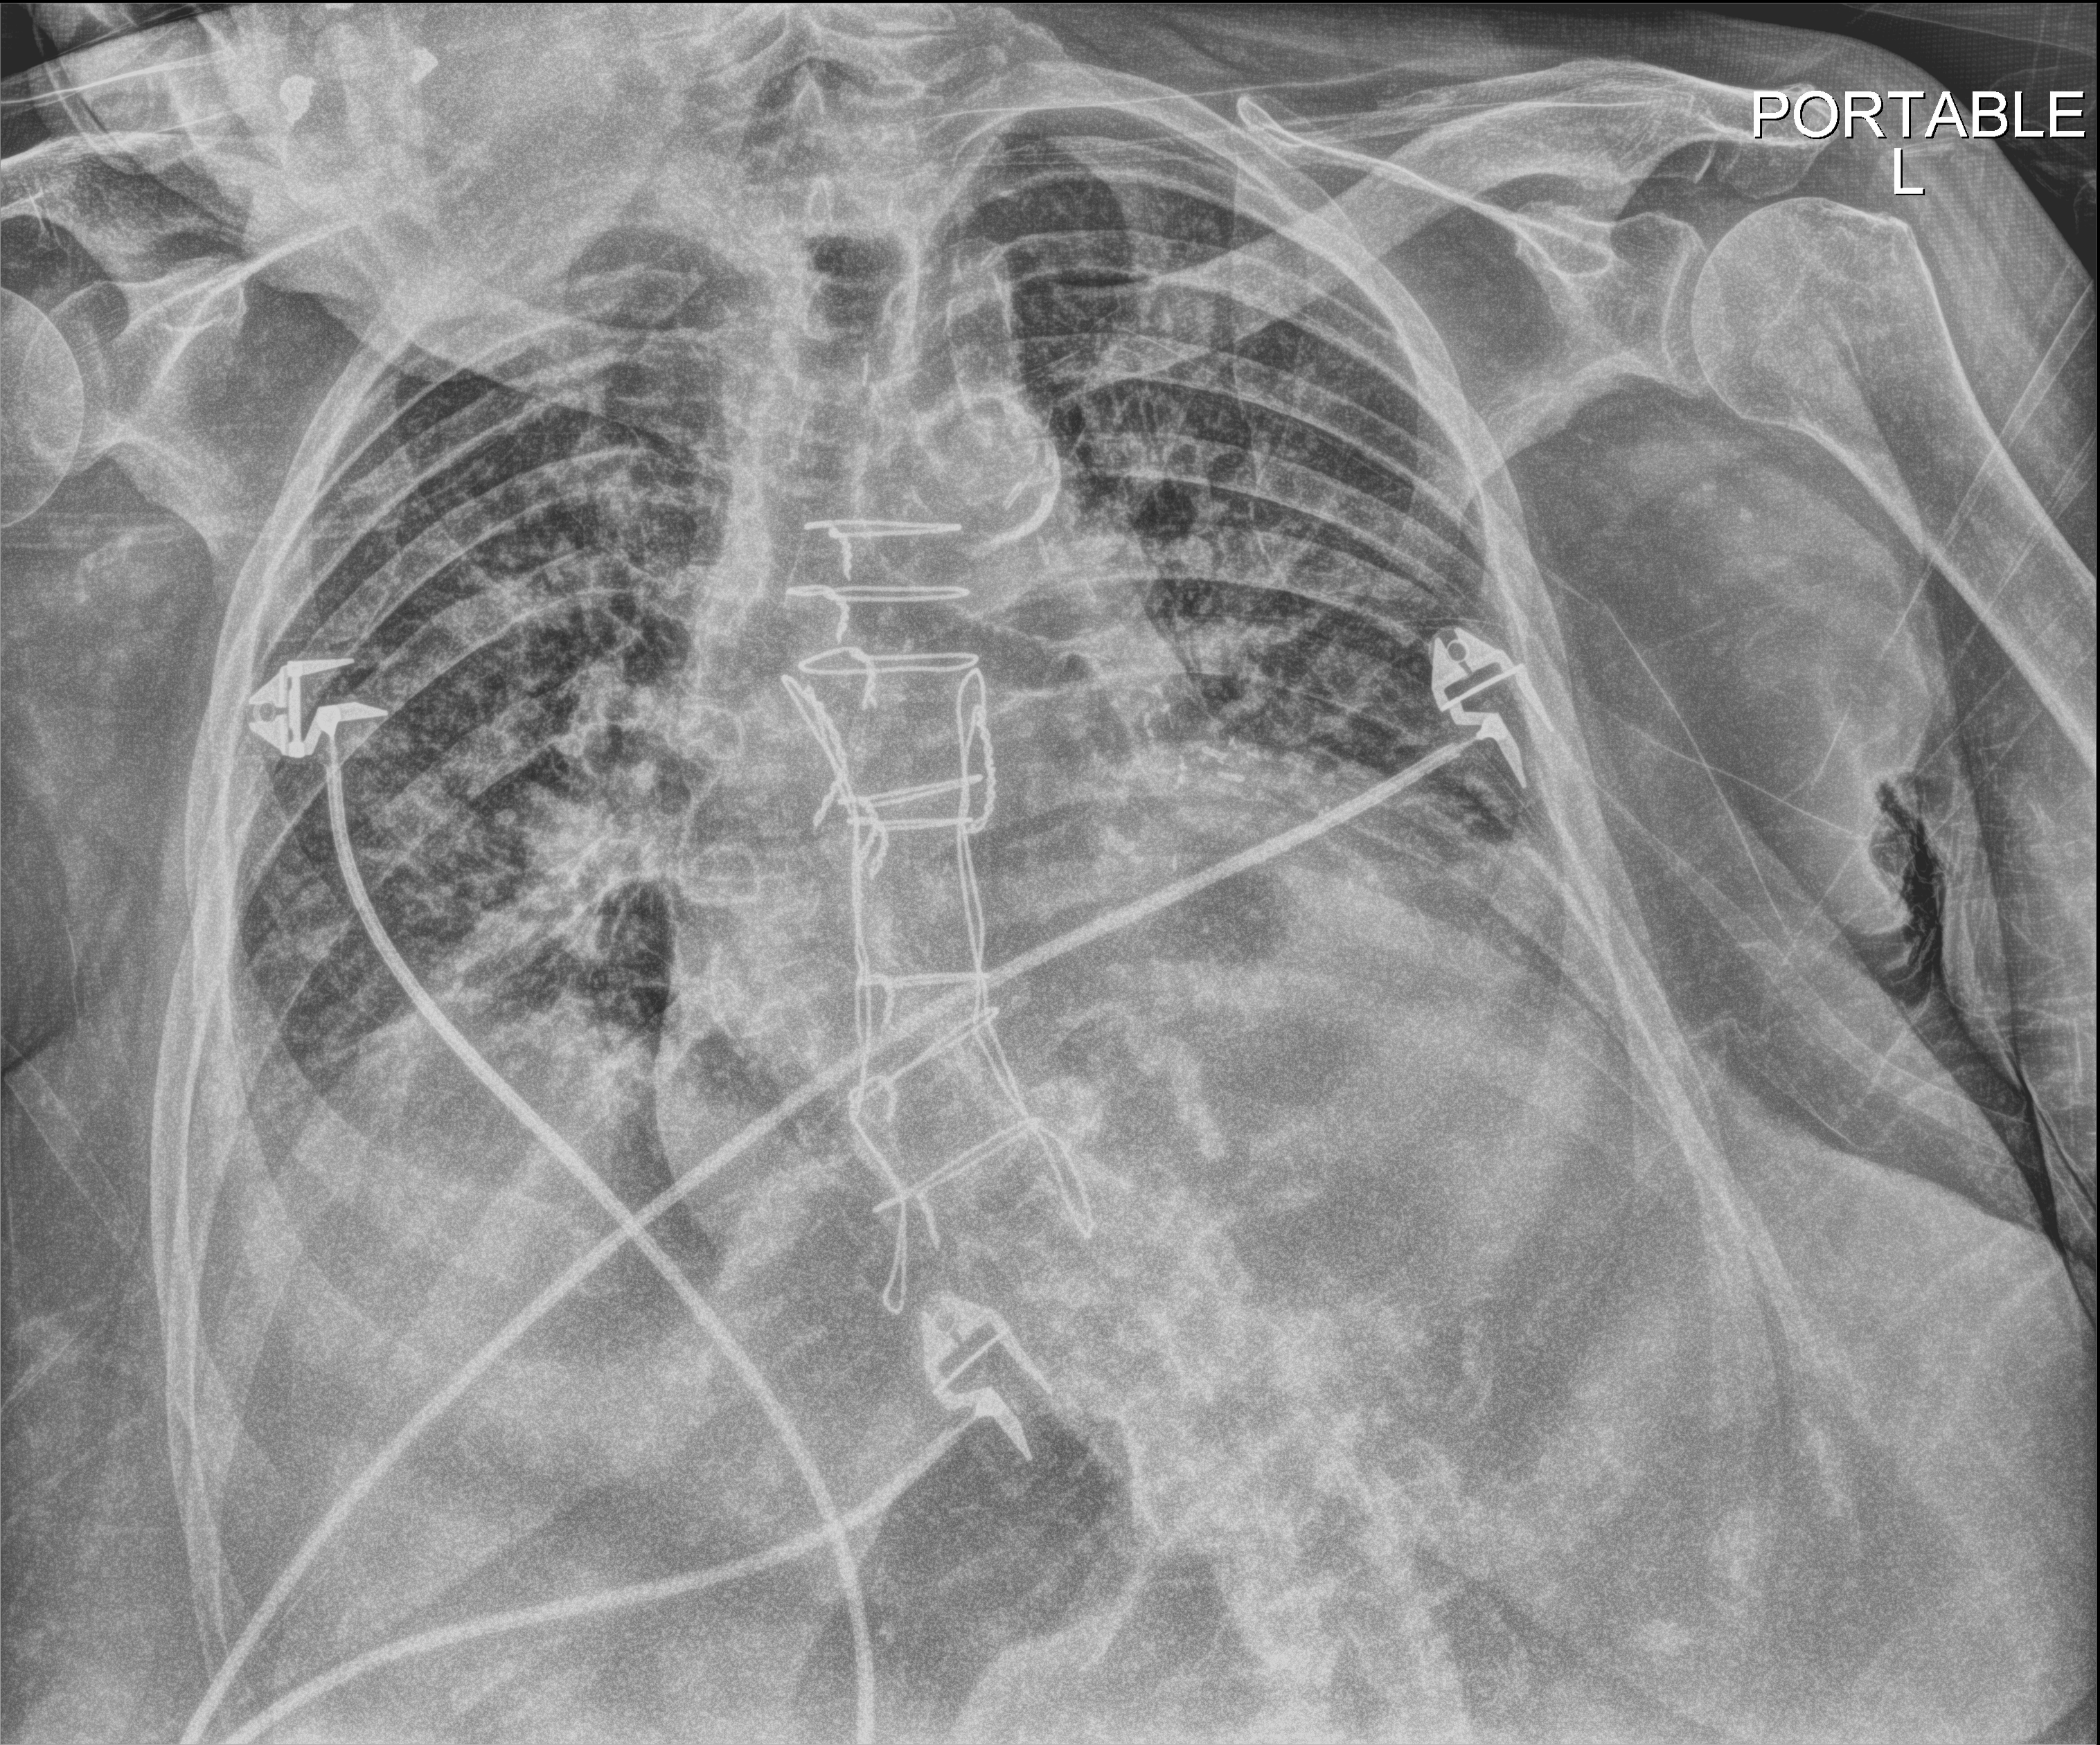
Chest radiograph; anteroposterior (AP) projection. Female patient hospitalised with COVID-19, age 75–90 years.
Admission-level facts for this patient (not findings on this image; timing relative to this image not recorded): admitted to intensive care during this hospital stay: no; mechanically ventilated during this hospital stay: no.